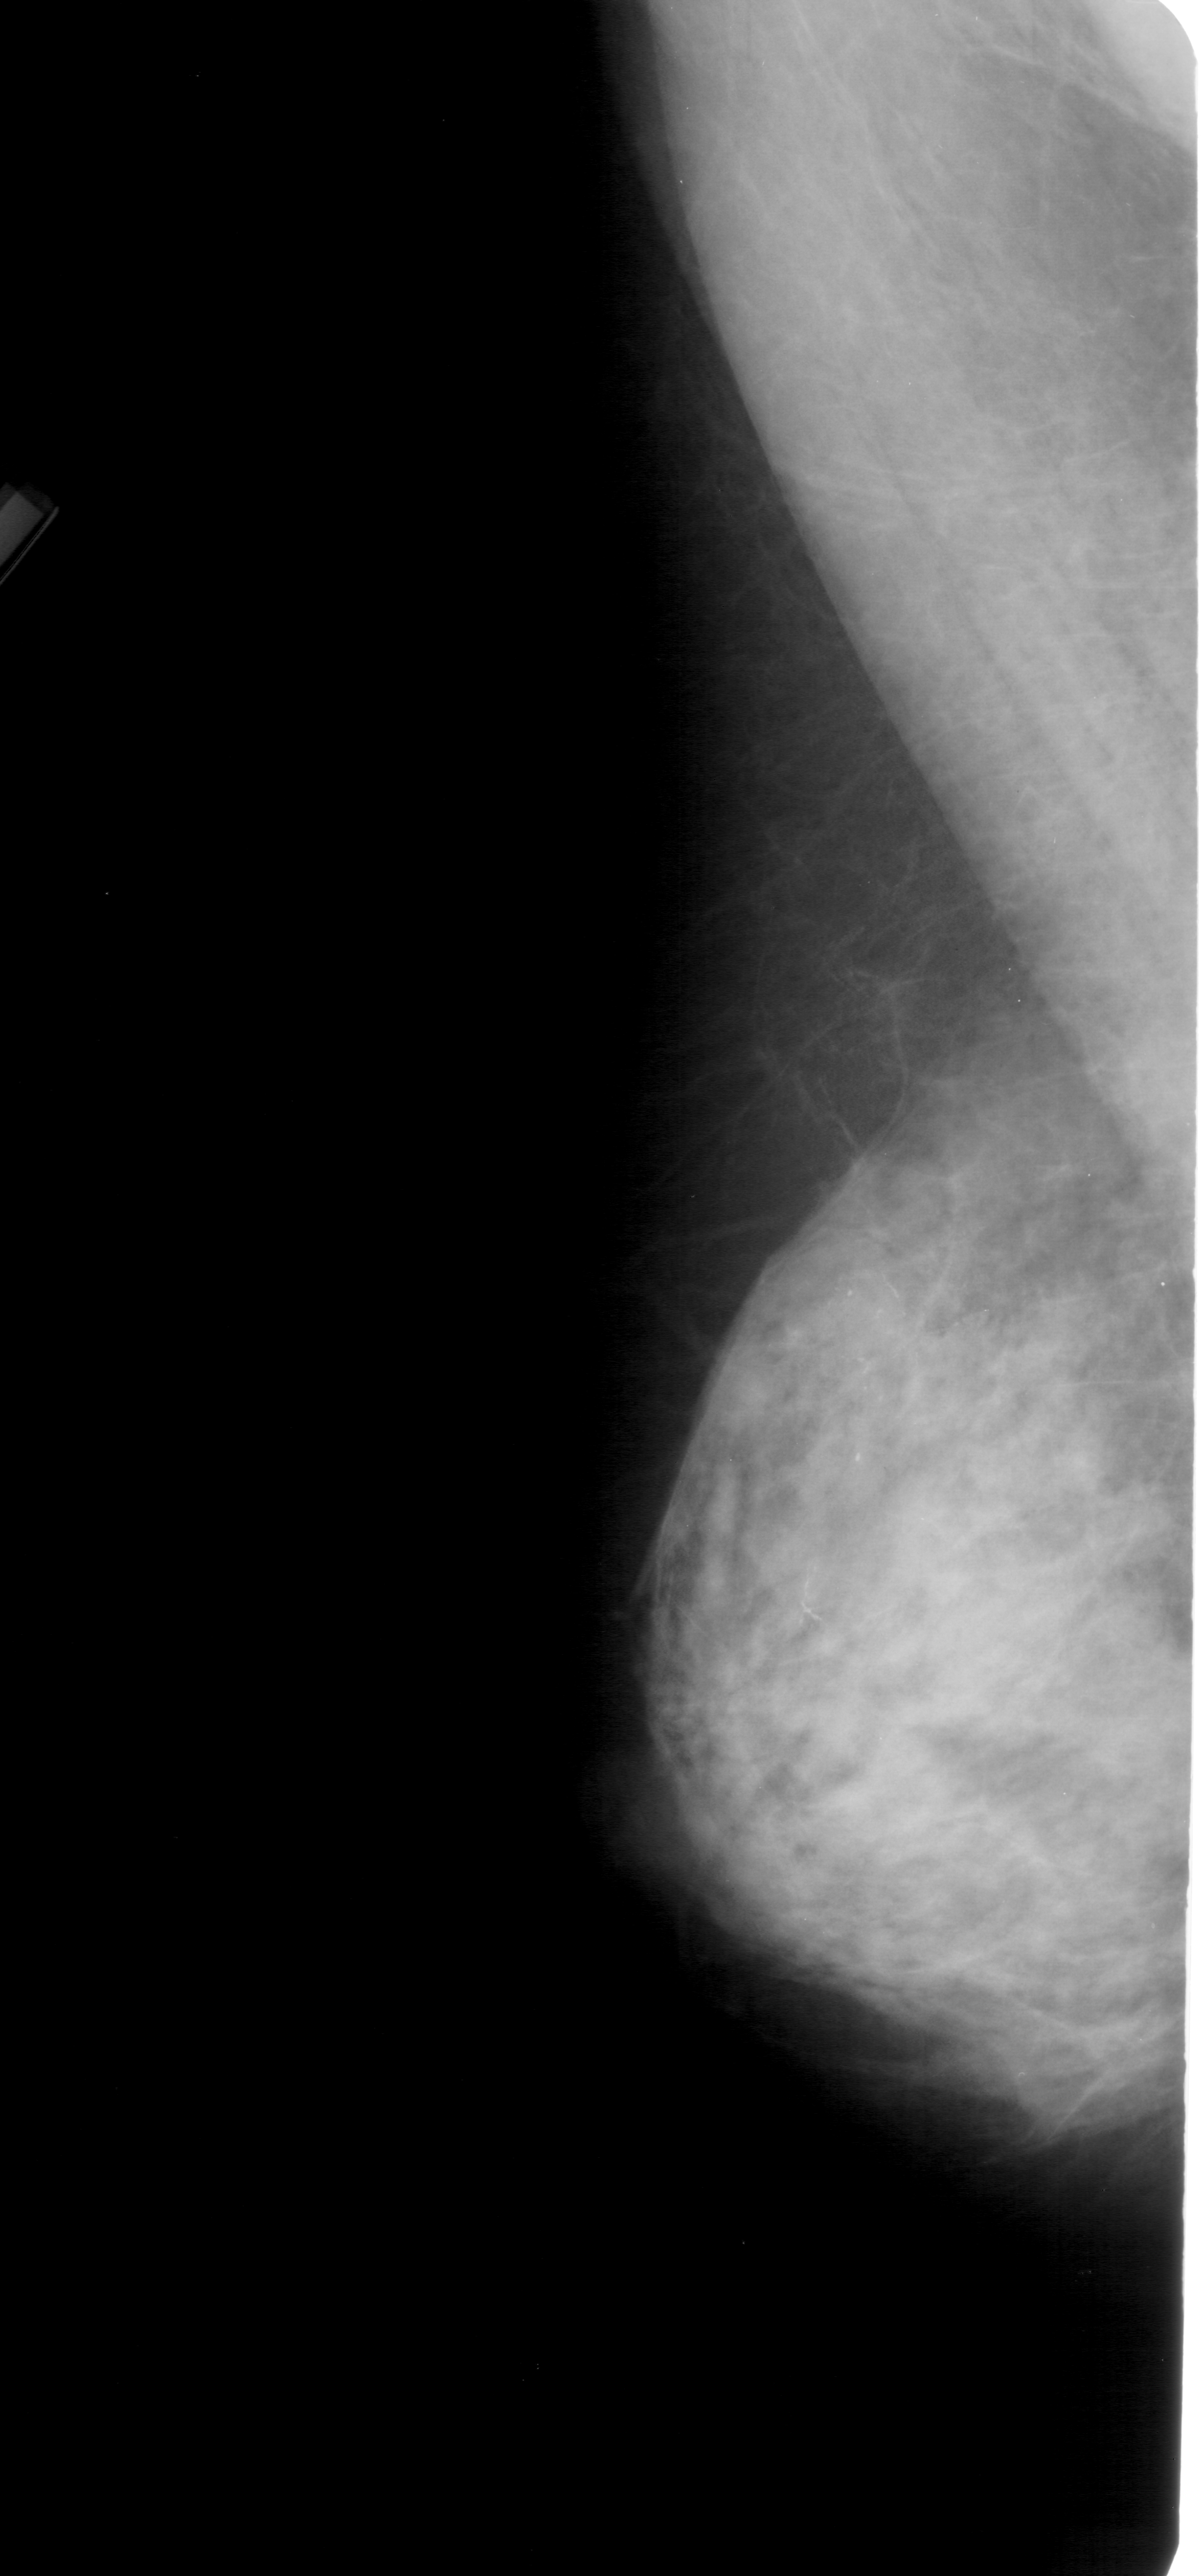
Mammogram (digitized film); left breast; MLO view; breast composition: extremely dense (BI-RADS density category 4 of 4).
- Calcifications, morphology pleomorphic, distribution segmental; BI-RADS assessment category 4; pathology result (as recorded, not read from the image): malignant.